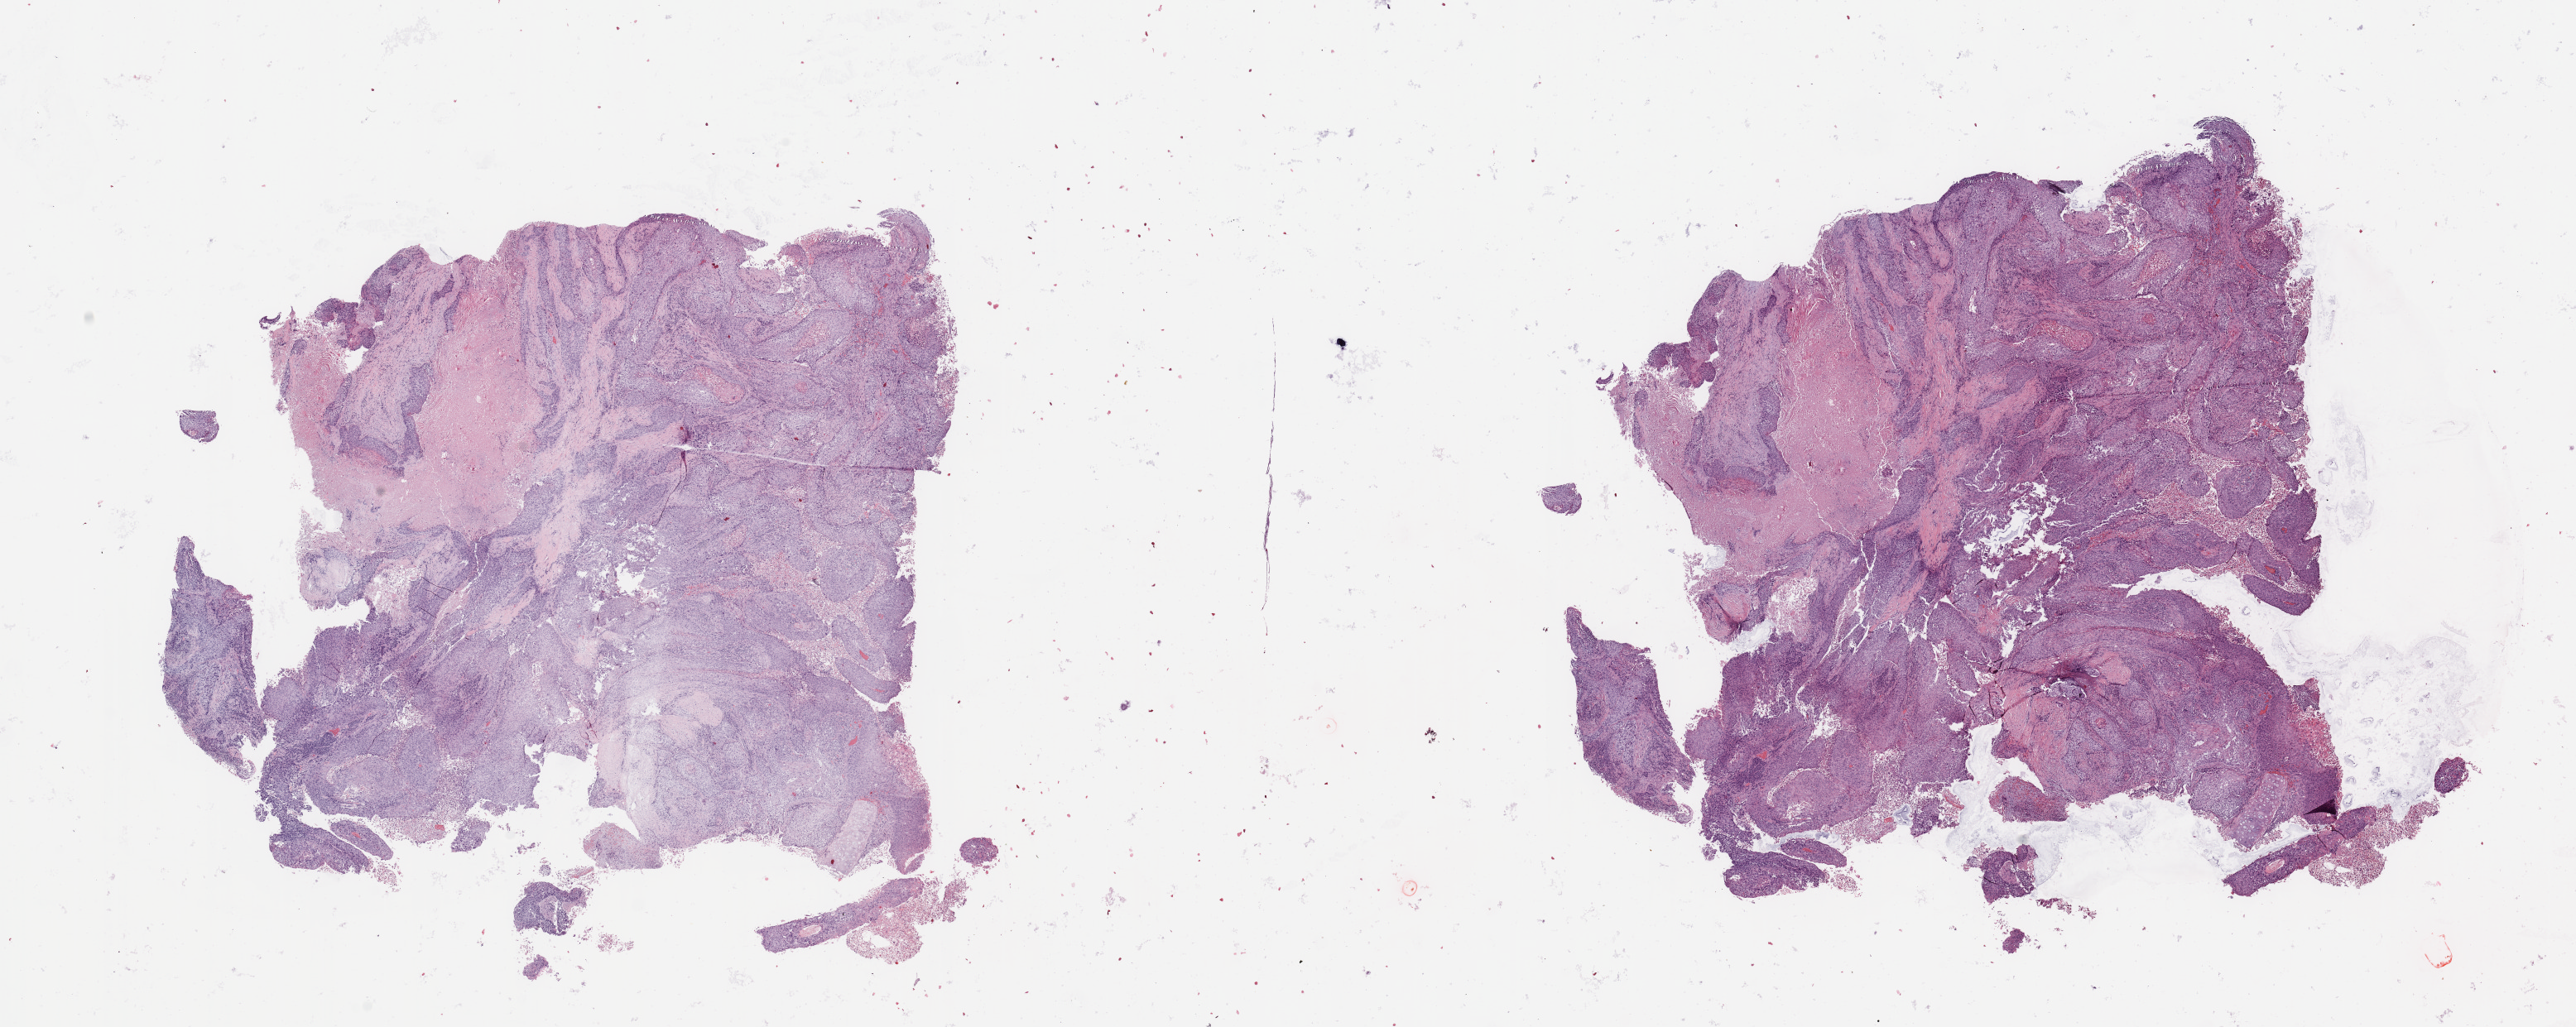
Digitized H&E-stained tissue section (whole slide), a low-resolution overview of the entire scanned area, about 24.6 x 9.8 mm (acquisition: 20x scan), tumour tissue sample, lung. Patient: female, age 48 years. Histologic grade: G2 (moderately differentiated).
- diagnosis: Squamous cell carcinoma, NOS
- primary tumour site (as recorded): left upper lobe
- AJCC pathologic stage: IB